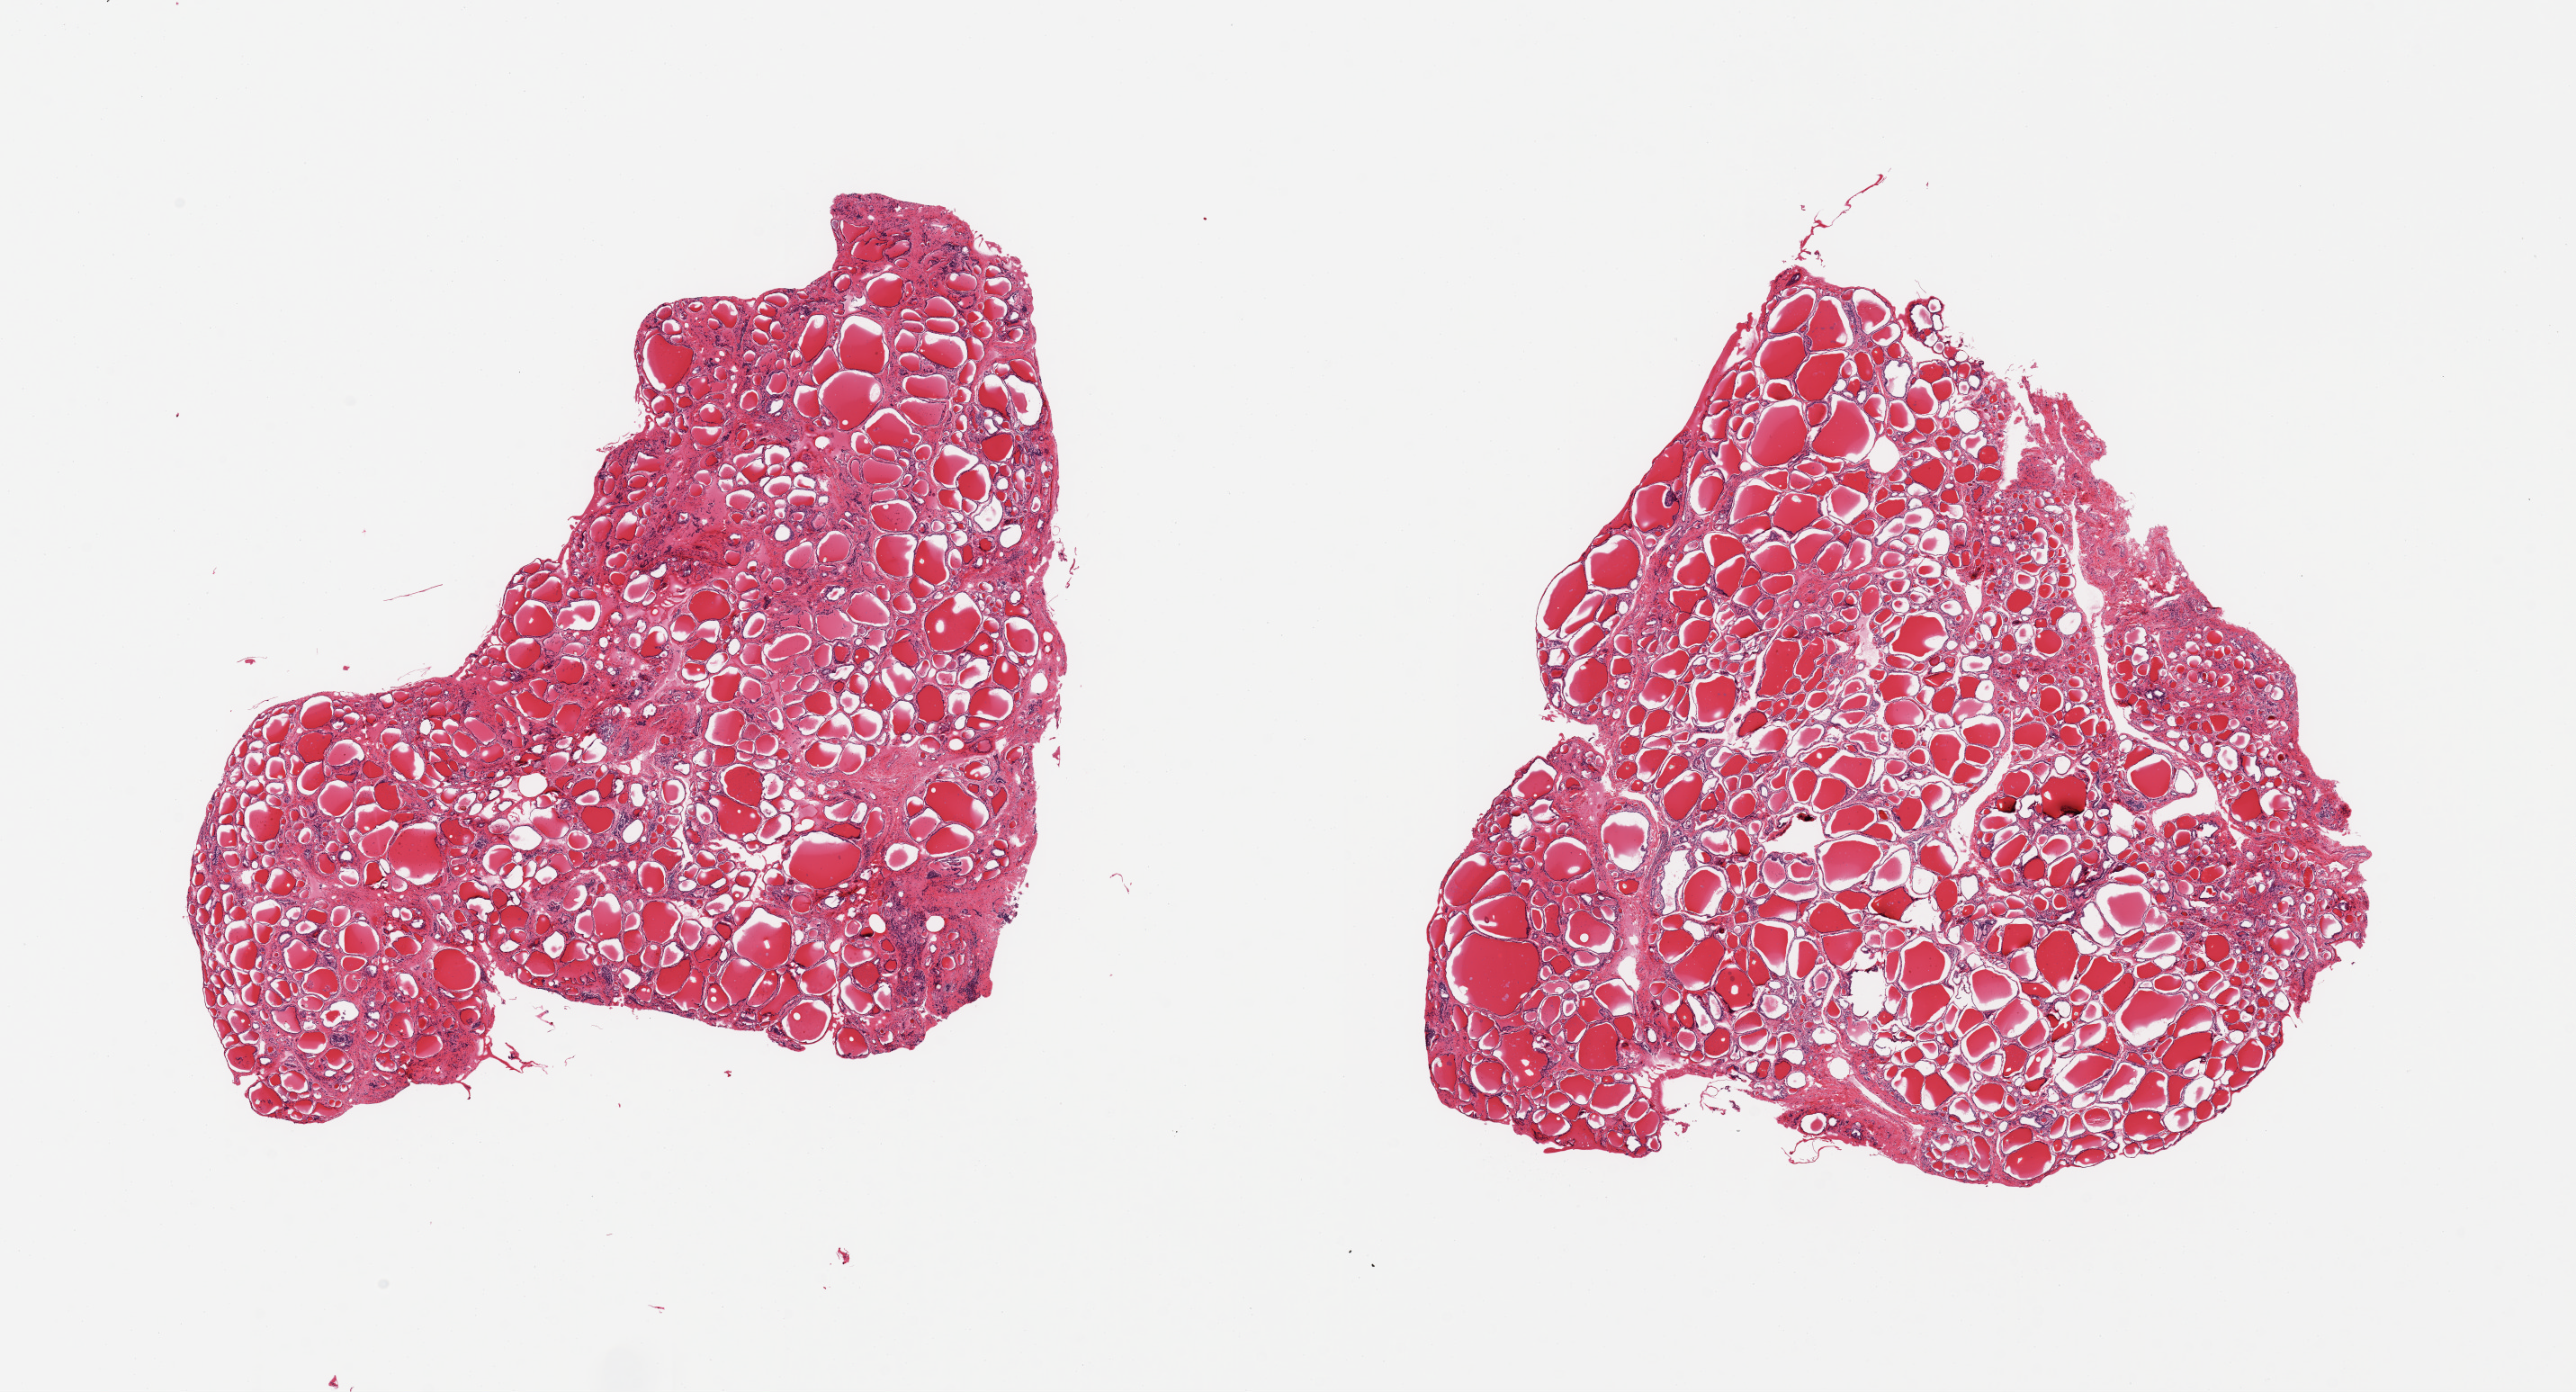
Whole-slide image, haematoxylin and eosin stain — low-resolution overview of the scanned area, about 22.6 x 12.2 mm (from a 20x scan). PAXgene-fixed paraffin-embedded (PFPE) section. Section of thyroid (target tissue). Donor tissue sample.
Reviewer comment on this tissue sample: 2 pieces; mild interstitial fibrosis.